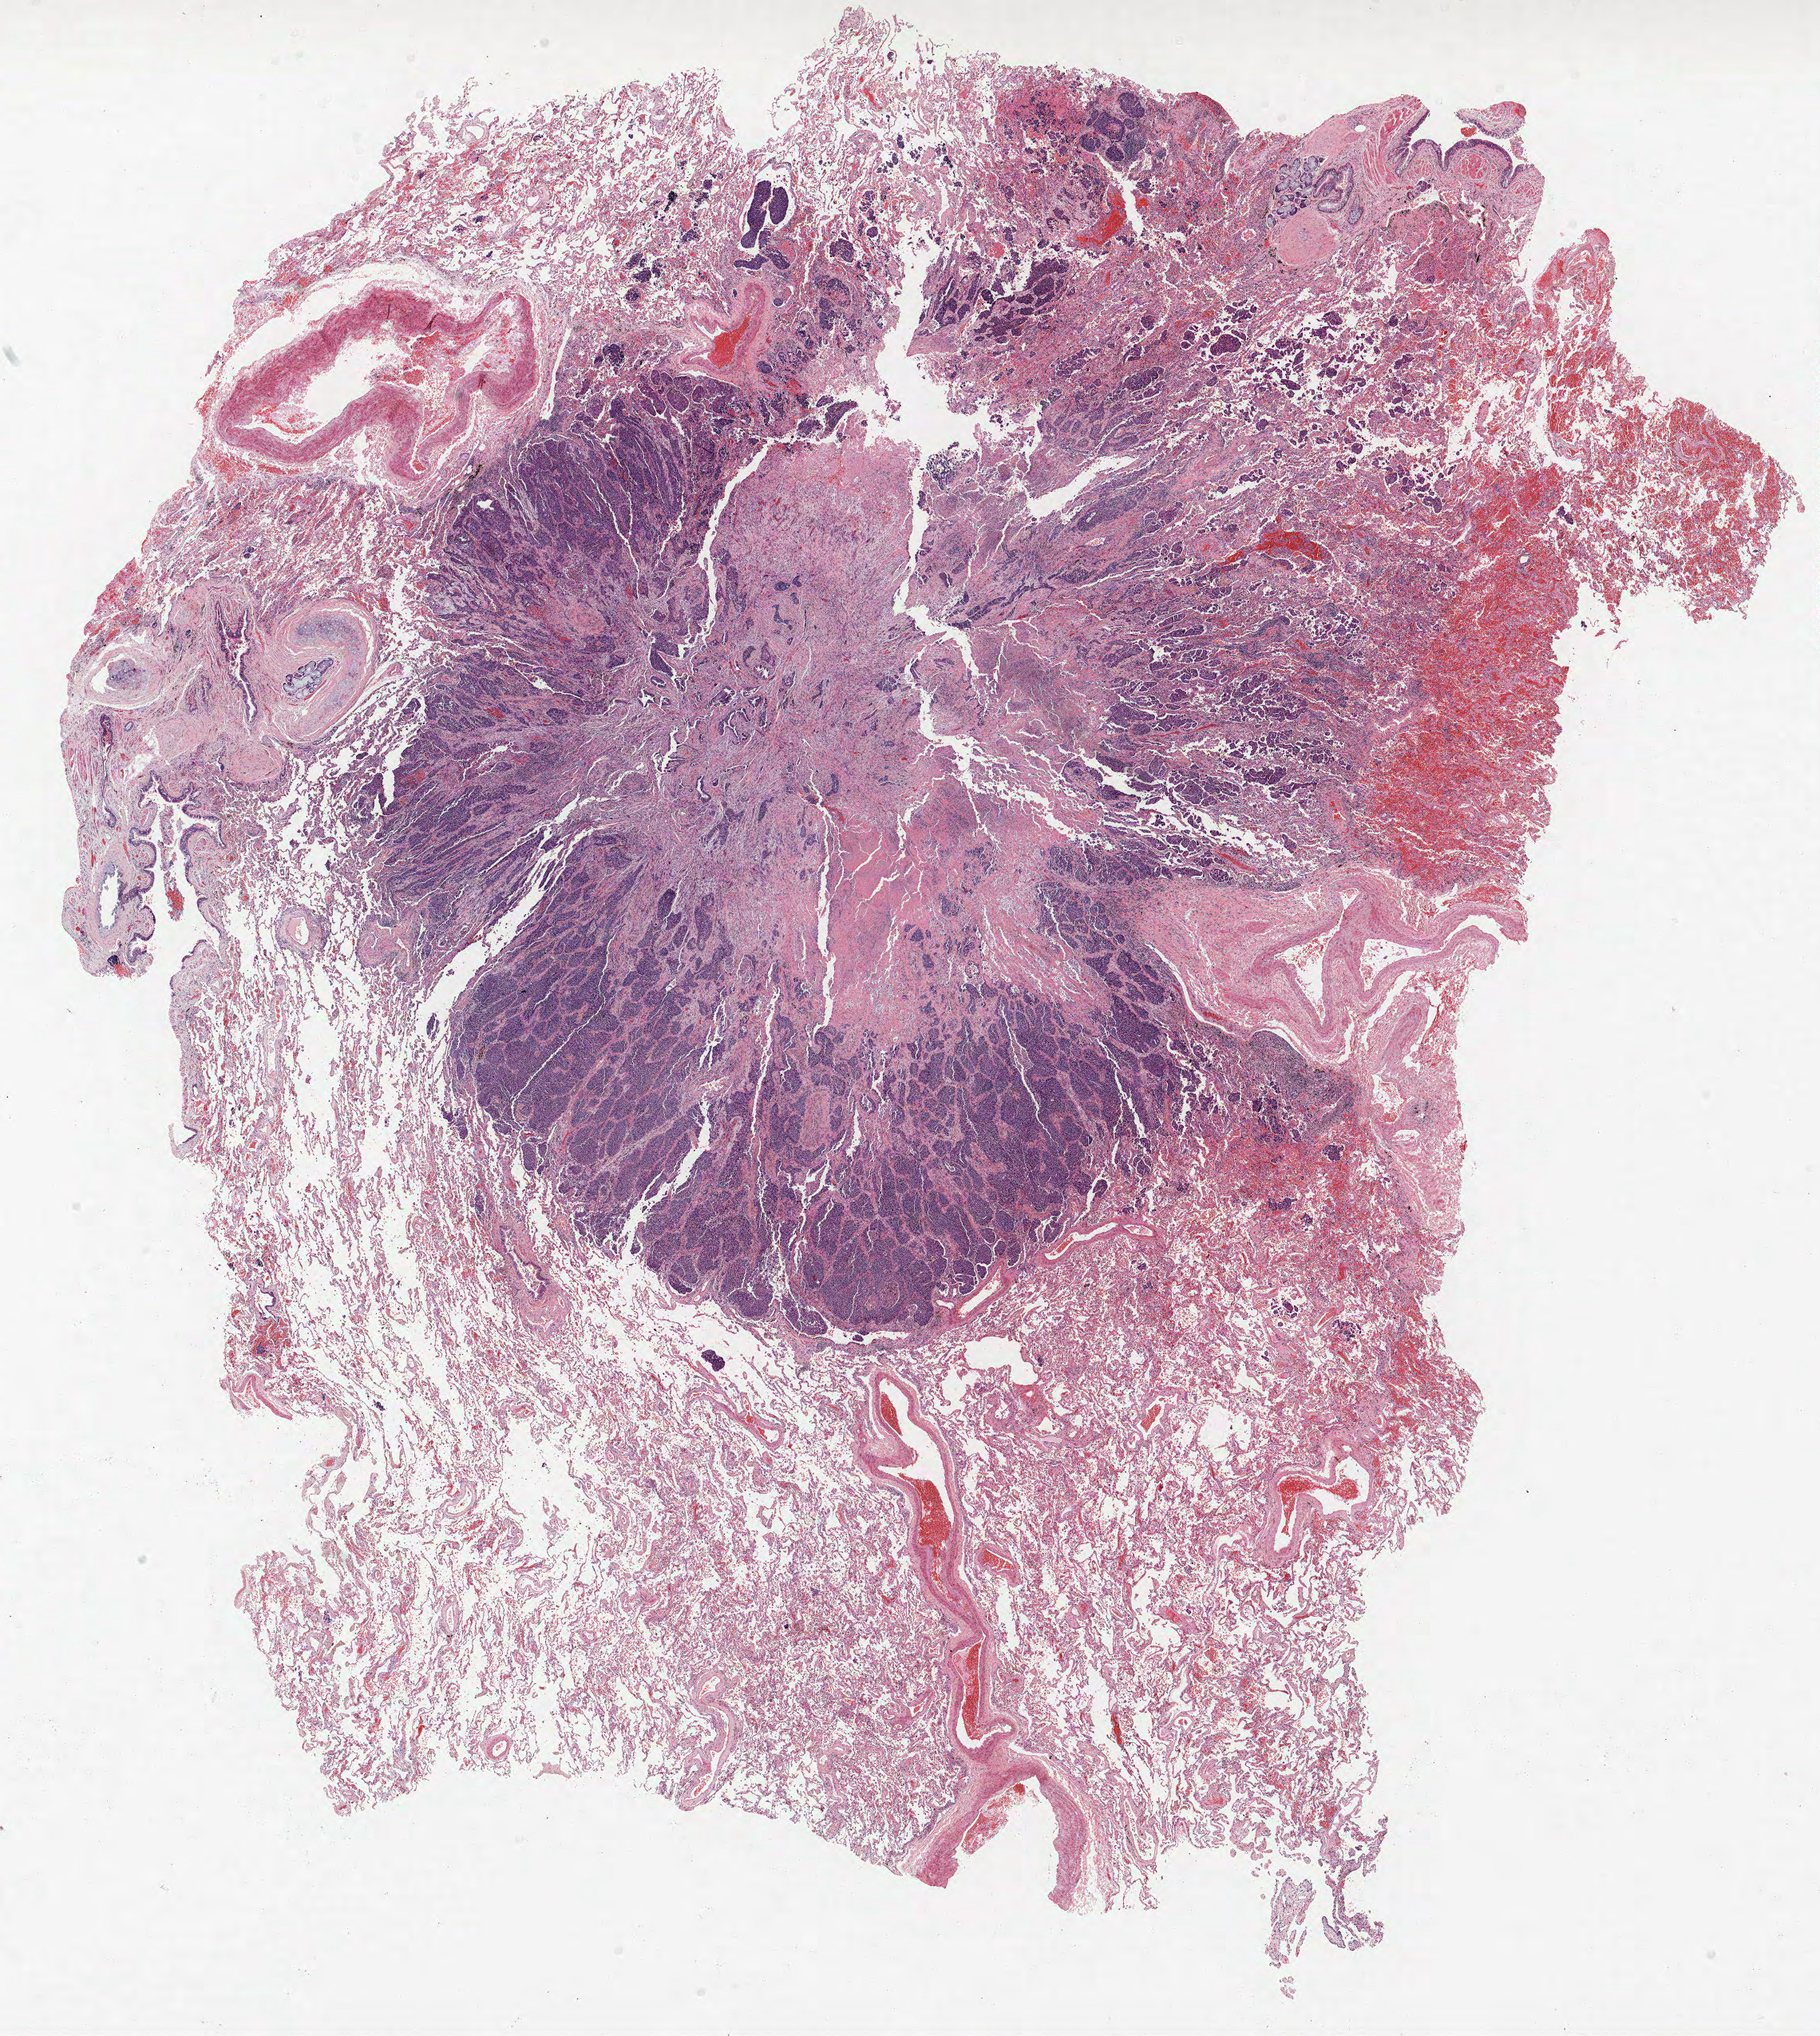
Whole-slide histology image, H&E-stained — shown as a low-resolution overview of the whole scanned area (about 18.2 x 20.4 mm); formalin-fixed paraffin-embedded (FFPE) section; lung tissue. Male patient, aged 72 at enrolment. Current smoker at enrolment. Grade: moderately differentiated (G2).
Tumour size (pathology): 20 mm. Participant's lung-cancer diagnosis: Squamous cell carcinoma, NOS. Primary tumour location (clinical record): left upper lobe. Stage (AJCC 6th edition): IA.